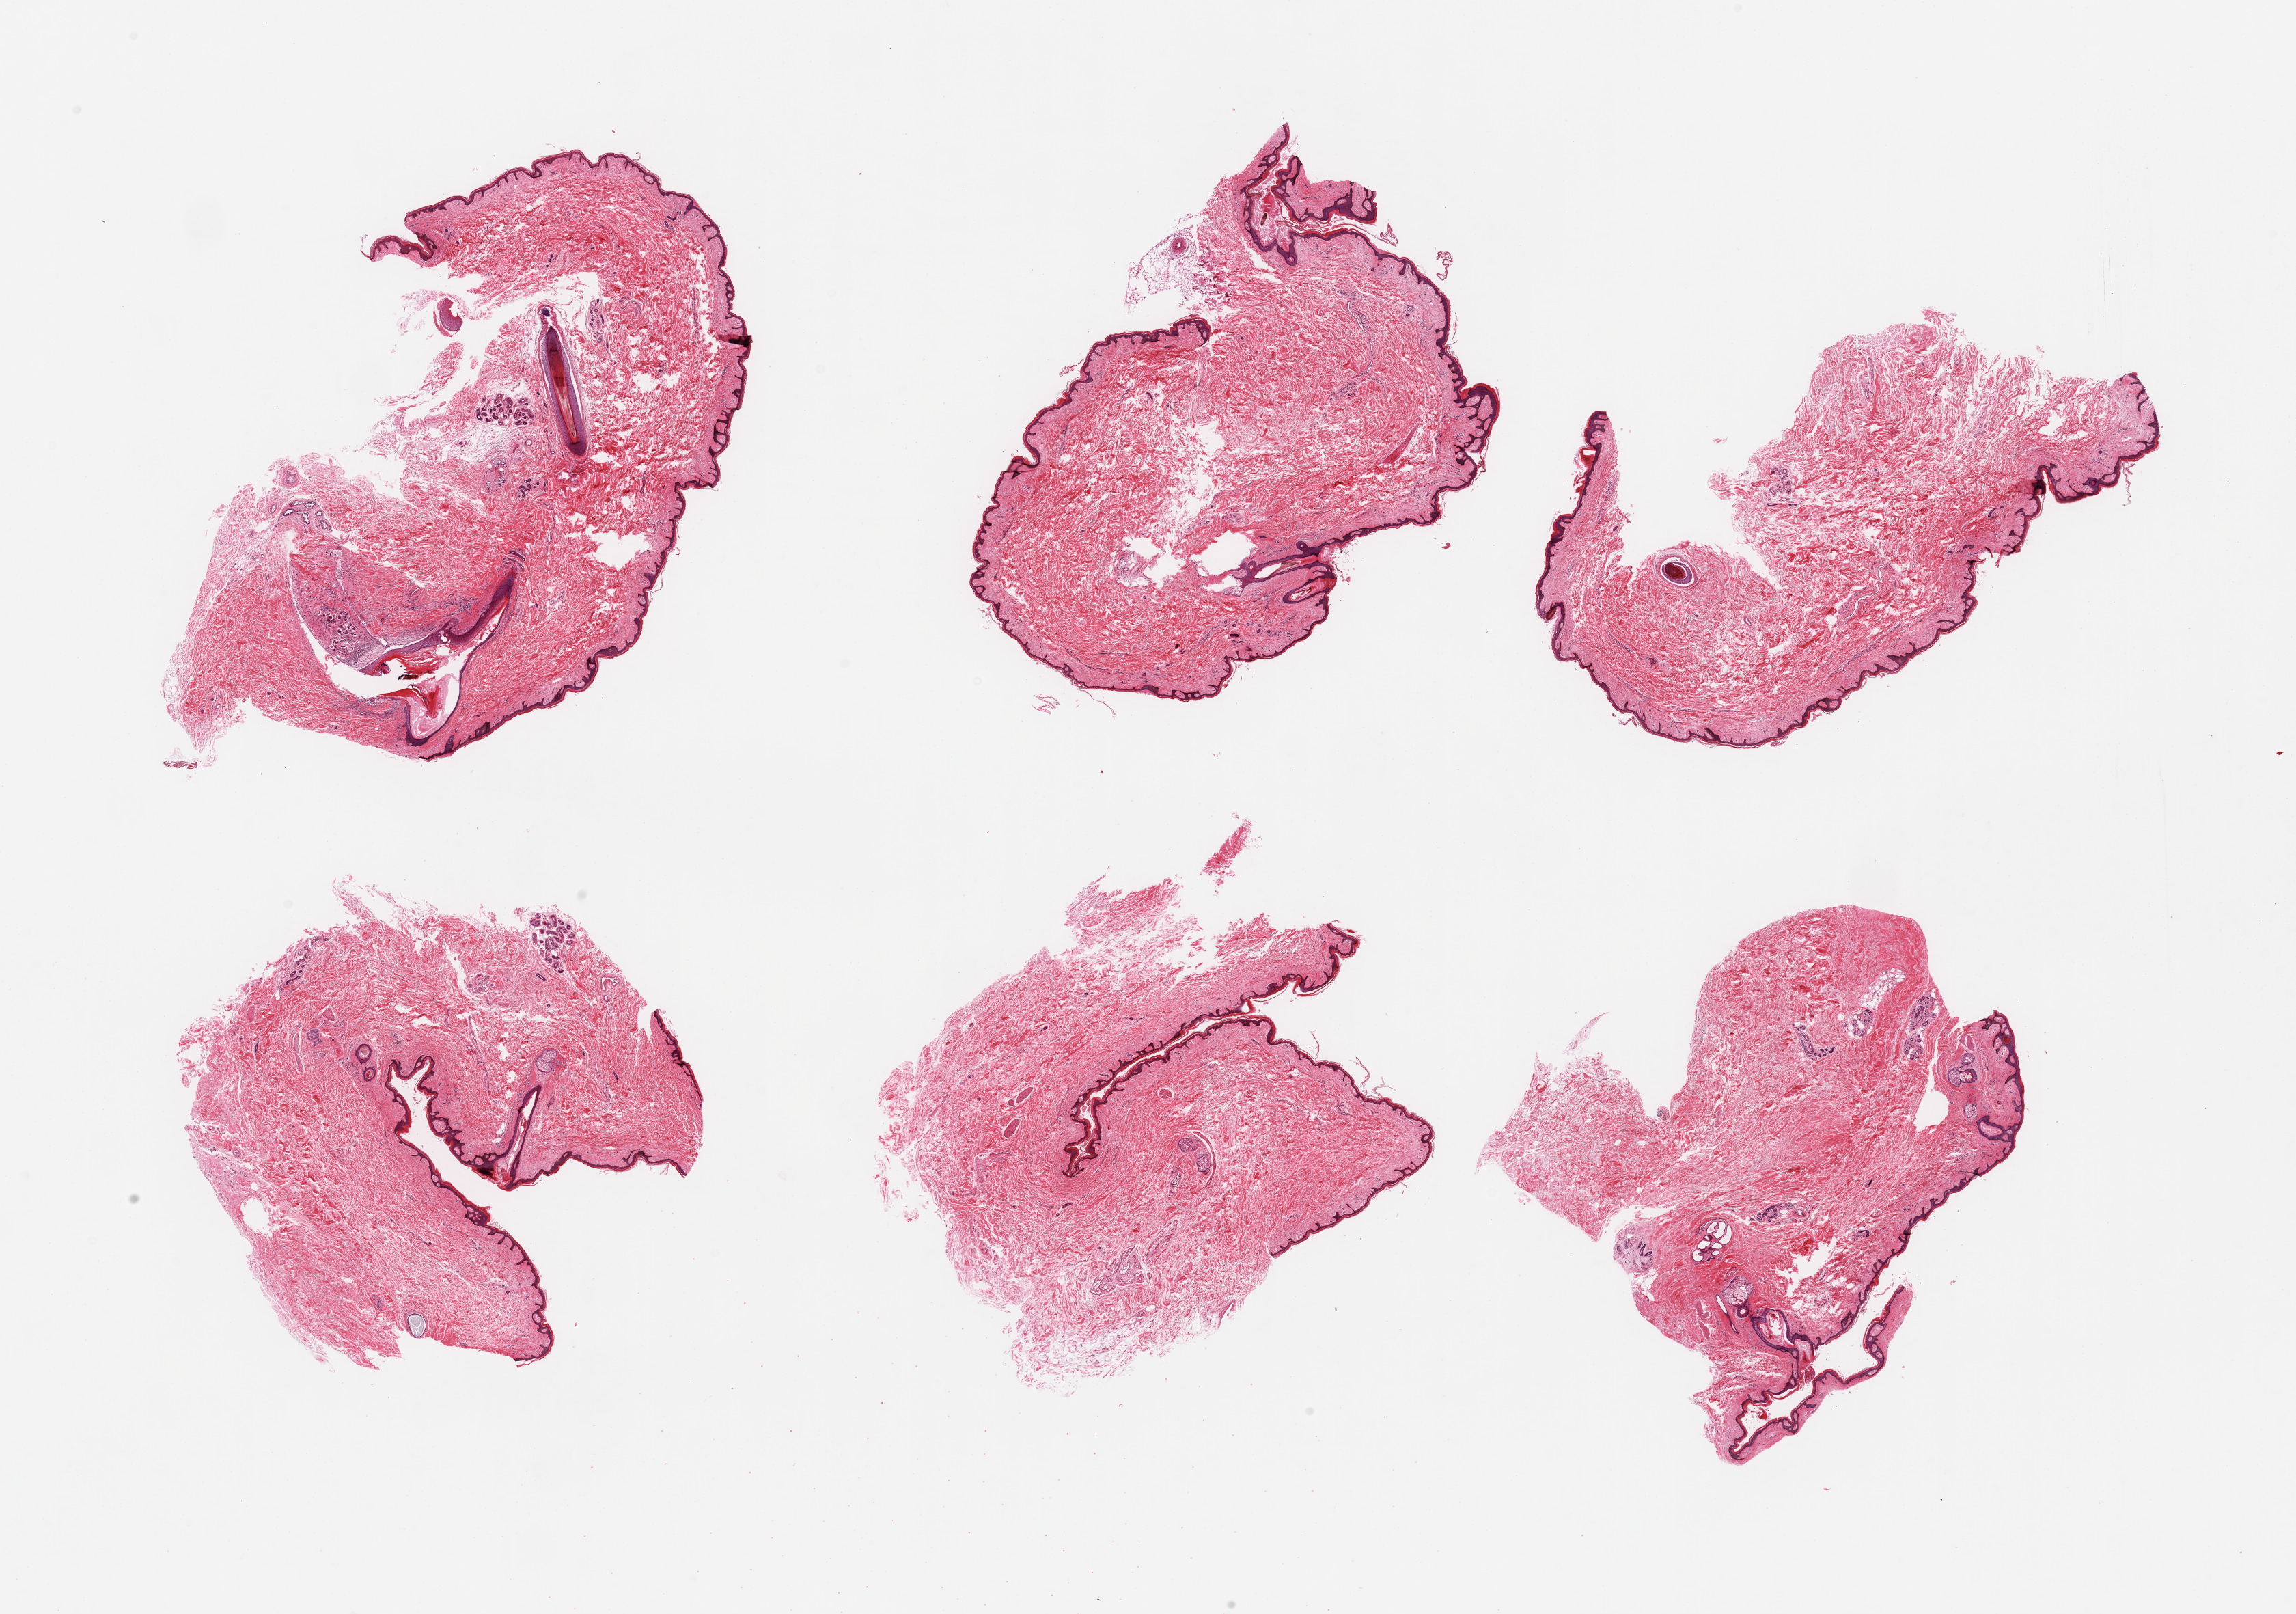
H&E whole-slide image, brightfield, low-resolution overview of the scanned area, about 26.6 x 18.7 mm (acquisition: 20x scan). PAXgene-fixed paraffin-embedded (PFPE) section. Target tissue: skin of suprapubic region. Donor tissue sample. Donor: male.
Pathologist's review note for this sample: 6 pieces, no dermal fat; squamous epithelium is ~30-40 microns.